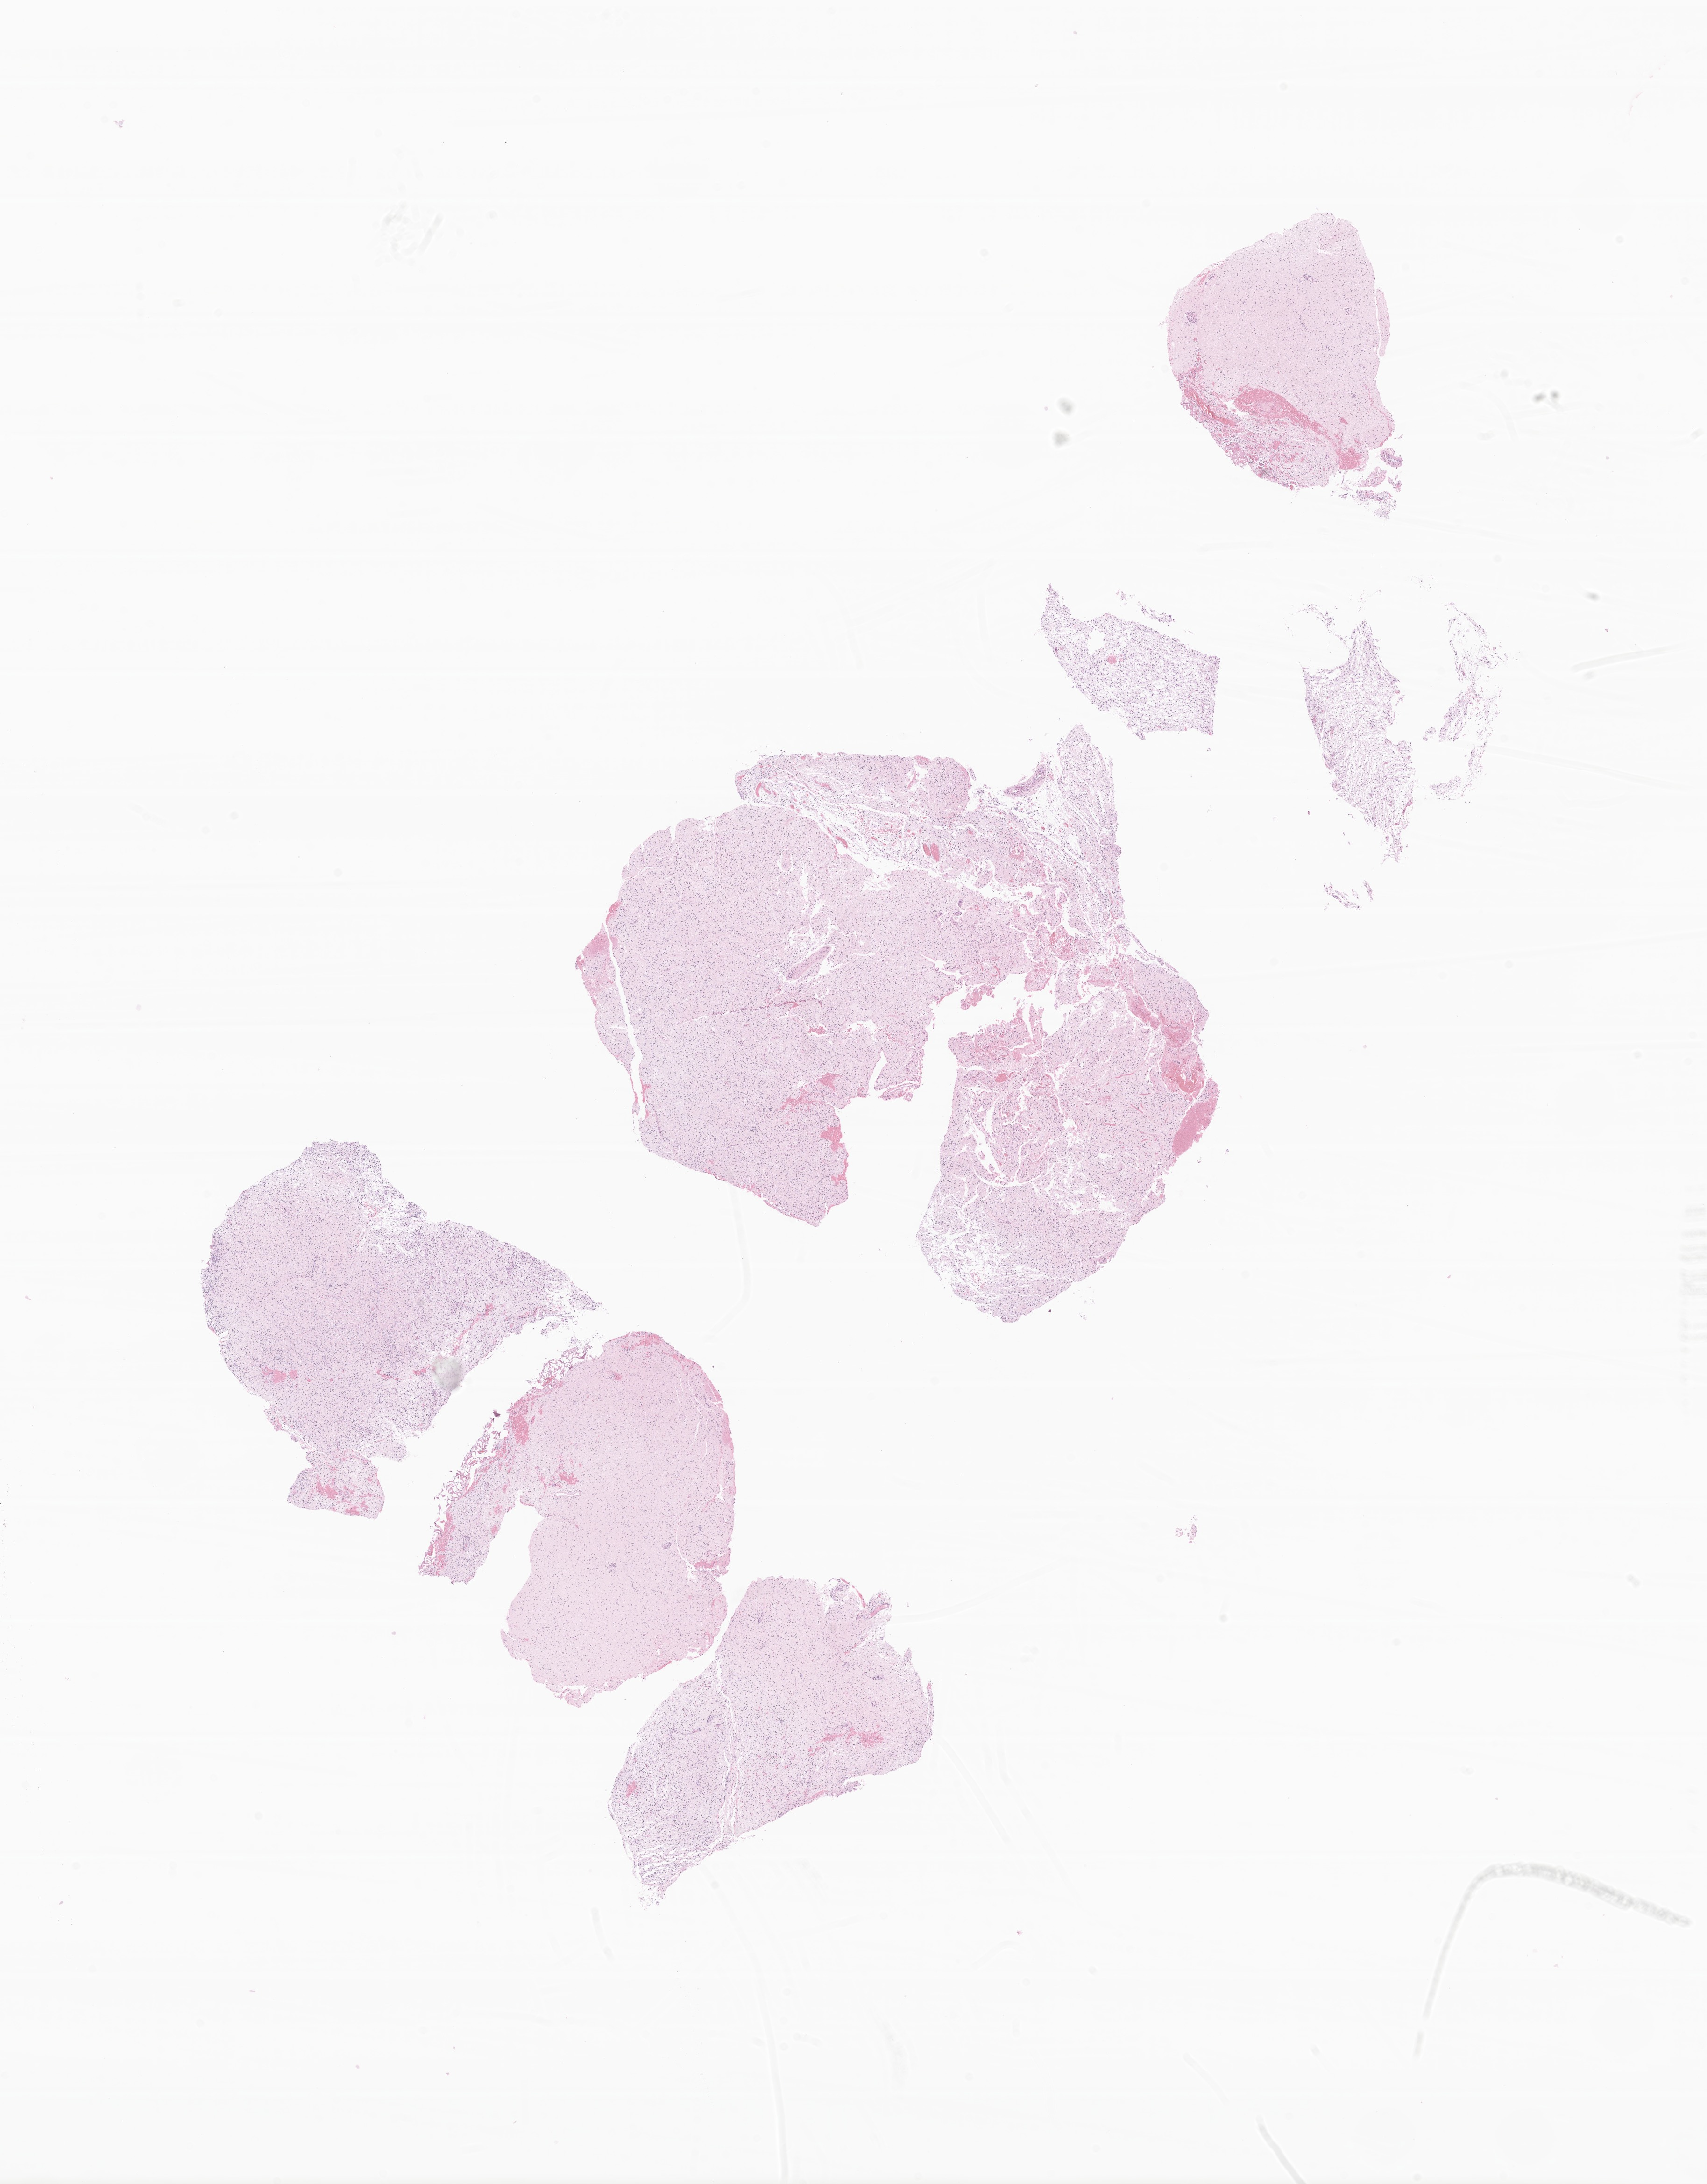
Whole-slide image, H&E stain of tumor tissue from the parietal lobe, whole scanned area (about 15.4 x 19.7 mm) shown as a low-resolution overview. Formalin-fixed, paraffin-embedded (FFPE) tissue. Patient: female, age 211 months (17 years 7 months).
Diagnosis (ICD-O-3 morphology term): Pilocytic astrocytoma.